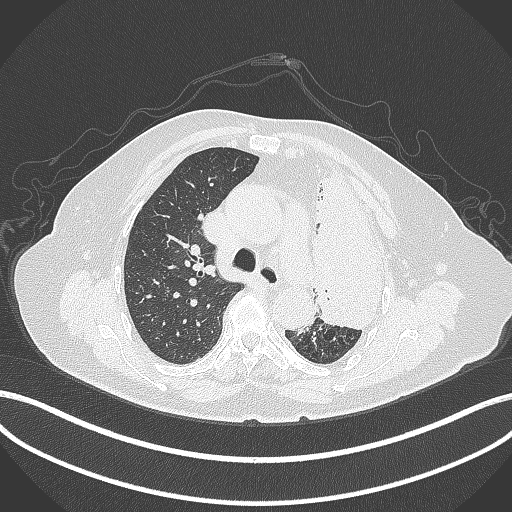
Chest CT, one axial slice; slice 270 of 399 in the series (ordered by position); 120 kVp; lung window (W 1500 / L -600 HU); 1 mm slice thickness; 512 × 512 image matrix, field of view 400 × 400 mm. Patient: female, 75 years. Case-level facts recorded for this patient, not image findings: clinical TNM (as recorded): T3 N3 M1.
Annotated regions visible in this slice (bounding box drawn by a radiologist):
- lung tumour (recorded histology: adenocarcinoma): box from (x=308, y=157) to (x=394, y=332) px